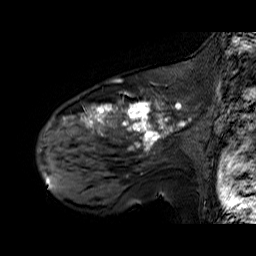
Breast MRI (dynamic contrast-enhanced), one sagittal slice; slice 44 of 60 in the series (ordered by position); dynamic contrast-enhanced series, time point 2 of 6 at this slice position (early post-contrast); 1.5 T; TE 6.3 ms, TR 32.9 ms; 256 × 256 image matrix. Female patient. From the clinical record (not read from this slice): setting: breast cancer imaged before/during neoadjuvant chemotherapy; receptor status: HER2-positive.
Annotated regions visible in this slice (semi-automatic segmentation, software-assisted and operator-edited):
- analysis volume of interest (the breast-tissue region the enhancement analysis was run in; not a lesion): bounding box (x1, y1, x2, y2) in pixels: (48, 92, 195, 174)
- tumour enhancement mask (voxels above the 100 % enhancement threshold inside the analysis volume of interest): (63, 100, 186, 150)